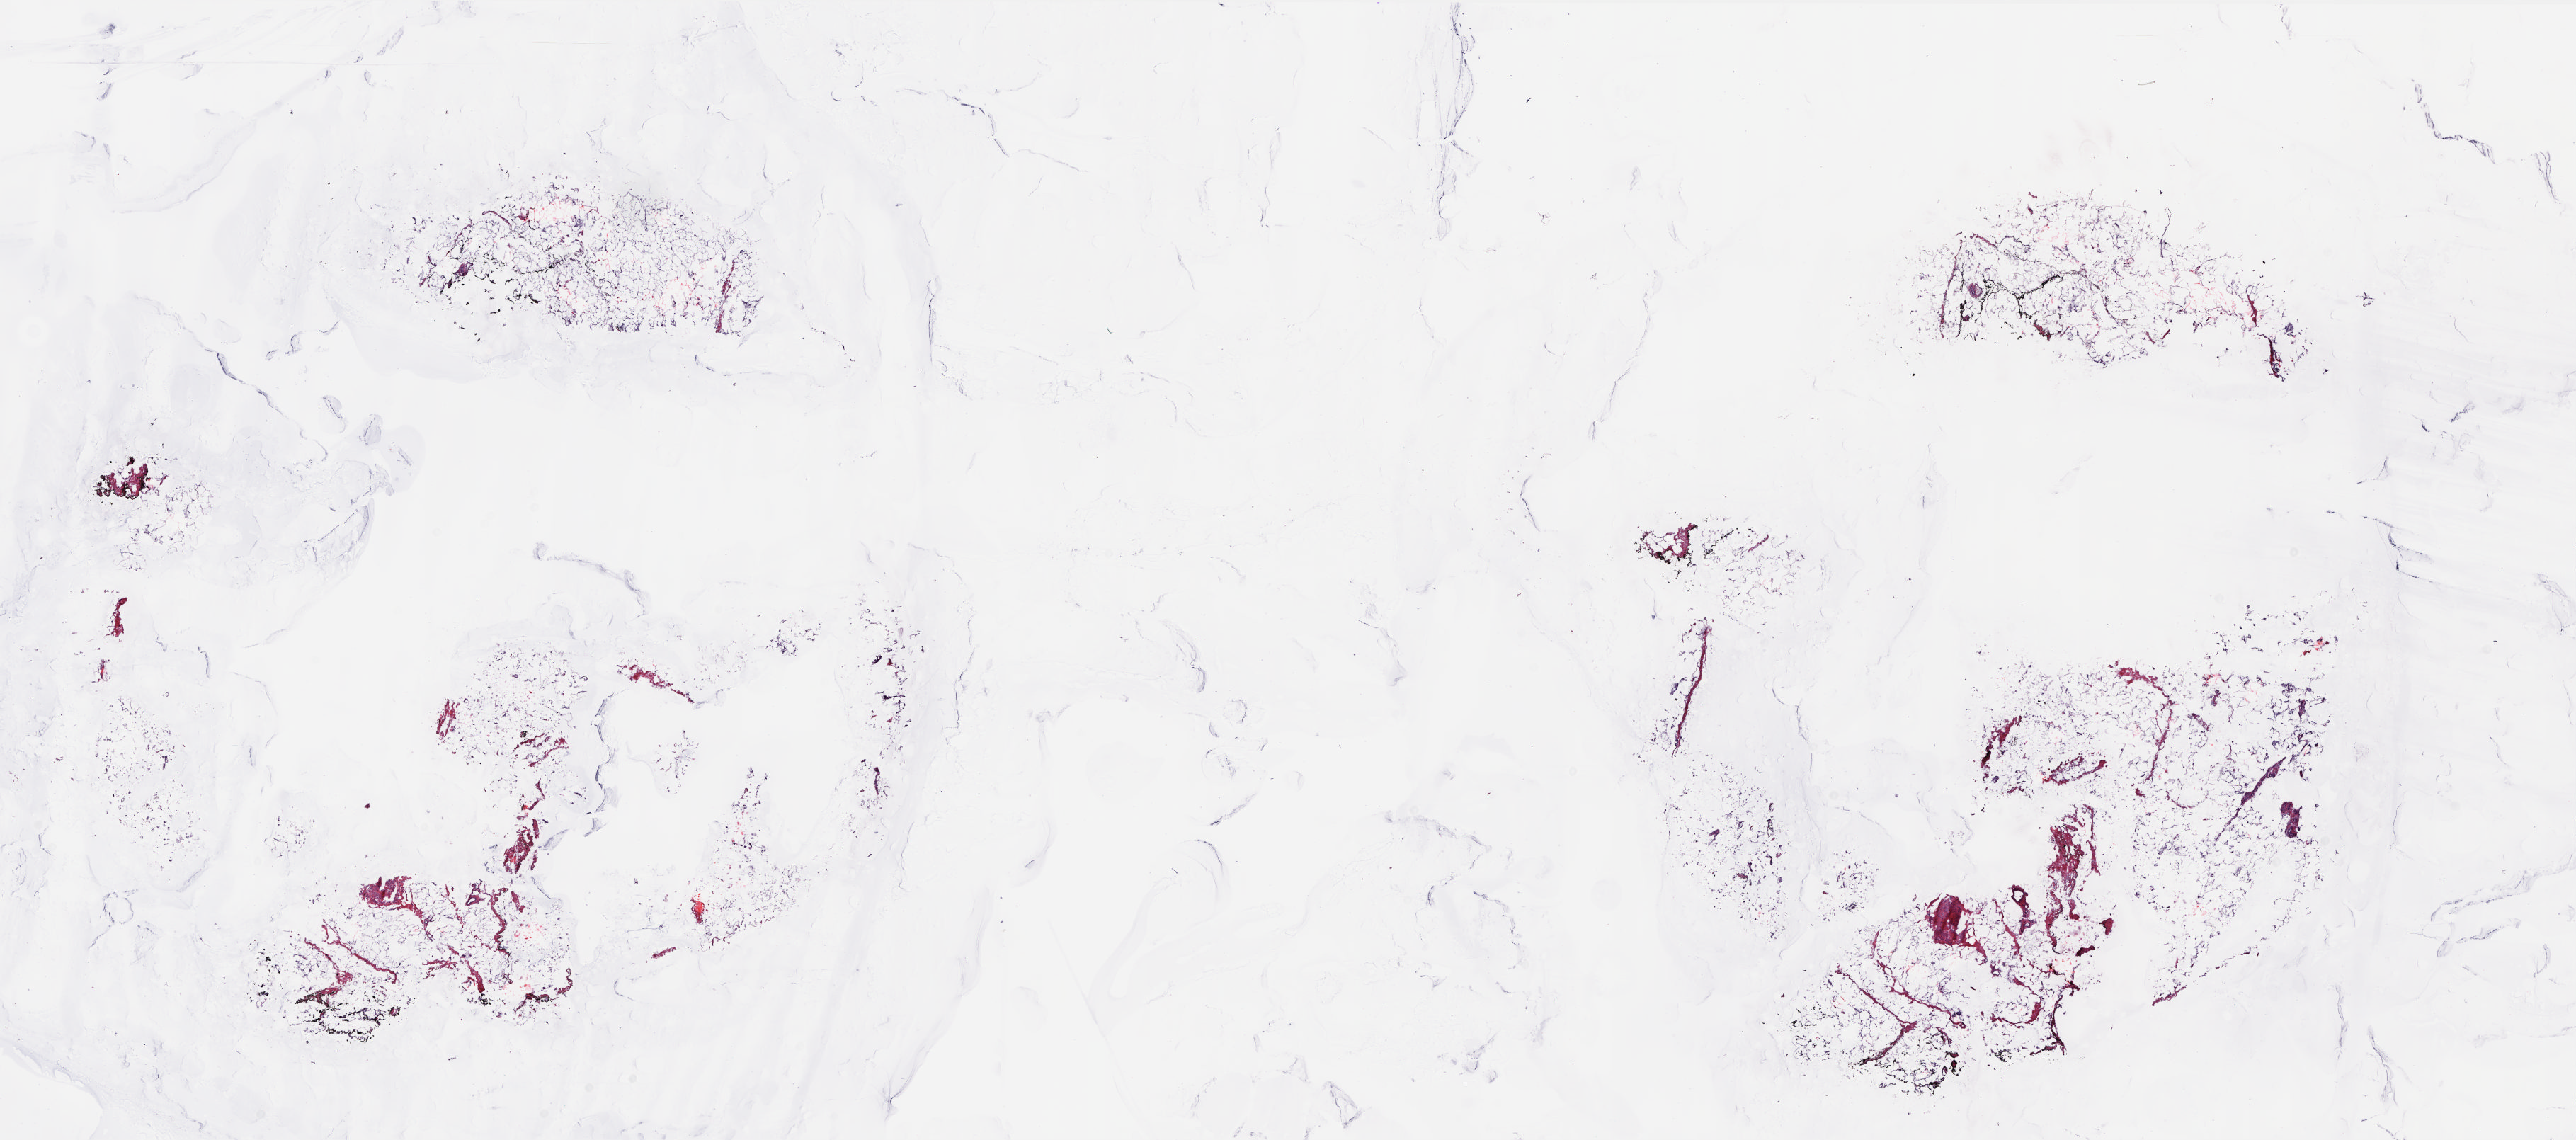
Digitized H&E-stained tissue section (whole slide) — whole scanned area (about 29.3 x 13.0 mm, slide scanned at 20x) shown as a low-resolution overview. Frozen section from the top of the tissue portion. Sample: solid tissue normal (non-tumour tissue), breast. Female patient; age at initial diagnosis 54 years. Pathologist review of this section (percent, as recorded): tumour cells 0%, tumour nuclei 0%, normal cells 0%, stromal cells 100%, necrosis 0%. Infiltration values recorded for this section: lymphocyte infiltration 0%, monocyte infiltration 0%, neutrophil infiltration 0%.
This section: solid tissue normal sample (biorepository sample class). Patient diagnosis: Infiltrating duct carcinoma, NOS.